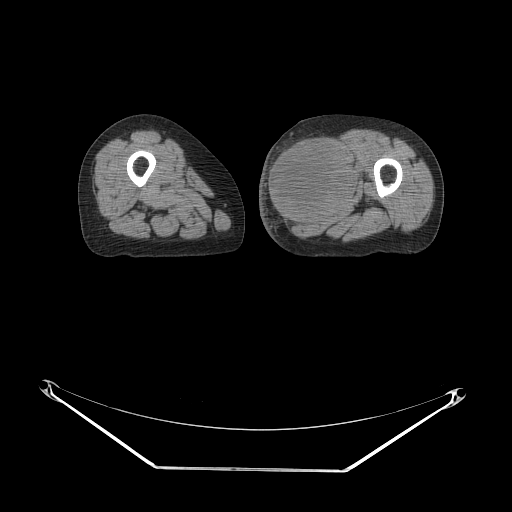
CT of an extremity soft-tissue mass (from a PET/CT study), one axial slice. Slice 29 of 91 in the series (ordered by position). Reconstruction kernel STANDARD. 140 kVp. Soft-tissue window (W 400 / L 40 HU). 512 × 512 image matrix, field of view 500 × 500 mm. Female patient. Case-level facts recorded for this patient, not image findings: histological type: pleomorphic leiomyosarcoma; grade: high; site of the primary tumour: left thigh.
Annotated regions visible in this slice (expert contour drawn on MRI and transferred to this co-registered scan by the dataset authors):
- gross tumour volume including surrounding oedema: bounding box (x1, y1, x2, y2) in pixels: (265, 135, 357, 225)
- gross tumour volume (mass): (265, 135, 355, 225)